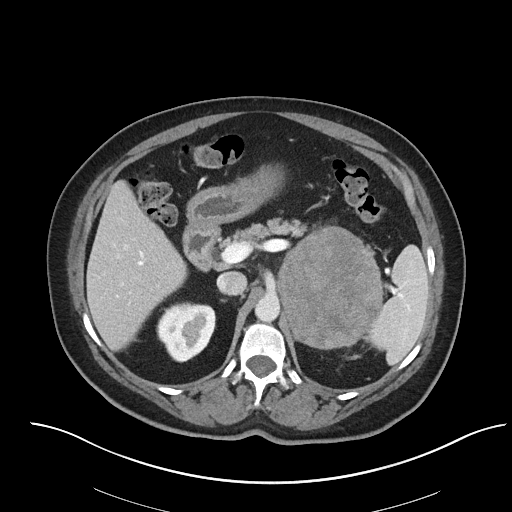
Contrast-enhanced abdominal CT, one axial slice. Position 49 of 92 along the scan axis. Reconstruction kernel I40f/2. 120 kVp. Intravenous contrast given. Soft-tissue window (W 400 / L 40 HU). 3 mm slice thickness. 512 × 512 image matrix, field of view 440 × 440 mm. Patient: female, 53 years. Case-level facts recorded for this patient, not image findings: diagnosis: adrenocortical carcinoma; tumour side: left adrenal; tumour size at pathology: 9 cm; Ki-67 index: 28 %; stage (as recorded): 2.
Outlined on this slice (semi-automatically segmented with operator editing):
- mass: bounding box <279,227,381,347> (left, top, right, bottom; pixels)